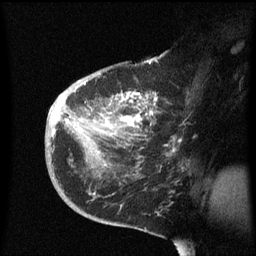
Breast MRI (dynamic contrast-enhanced), one sagittal slice; position 35 of 60 along the scan axis; dynamic contrast-enhanced series, image 2 of 3 at this slice position (ordered by acquisition); 1.5 T; TE 4.2 ms, TR 8.4 ms; 2.3 mm slice thickness; 256 × 256 image matrix. Patient: female, 38 years. From the clinical record (not read from this slice): setting: breast cancer imaged before/during neoadjuvant chemotherapy; receptor status: HER2-positive.
Outlined on this slice (semi-automatic segmentation, software-assisted and operator-edited):
- analysis volume of interest (the breast-tissue region the enhancement analysis was run in; not a lesion): bounding box [x1, y1, x2, y2] px = [45, 78, 188, 213]
- tumour enhancement mask (voxels above the 70 % enhancement threshold inside the analysis volume of interest): [53, 84, 175, 153]